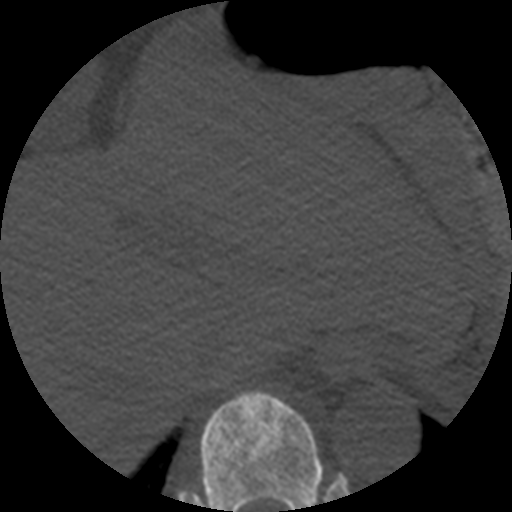
CT including the spine, one axial slice; slice 271 of 508 in the series (ordered by position); bone window (W 1800 / L 400 HU); 1.25 mm slice thickness; 512 × 512 image matrix, field of view 160 × 160 mm. Patient age 57 years. Case-level facts recorded for this patient, not image findings: primary cancer: prostate.
Outlined on this slice (semi-automatic segmentation, software-assisted and operator-edited):
- T10 vertebra: box from (x=200, y=391) to (x=323, y=512) px
- T9 vertebra: (x=243, y=473)–(x=323, y=506)